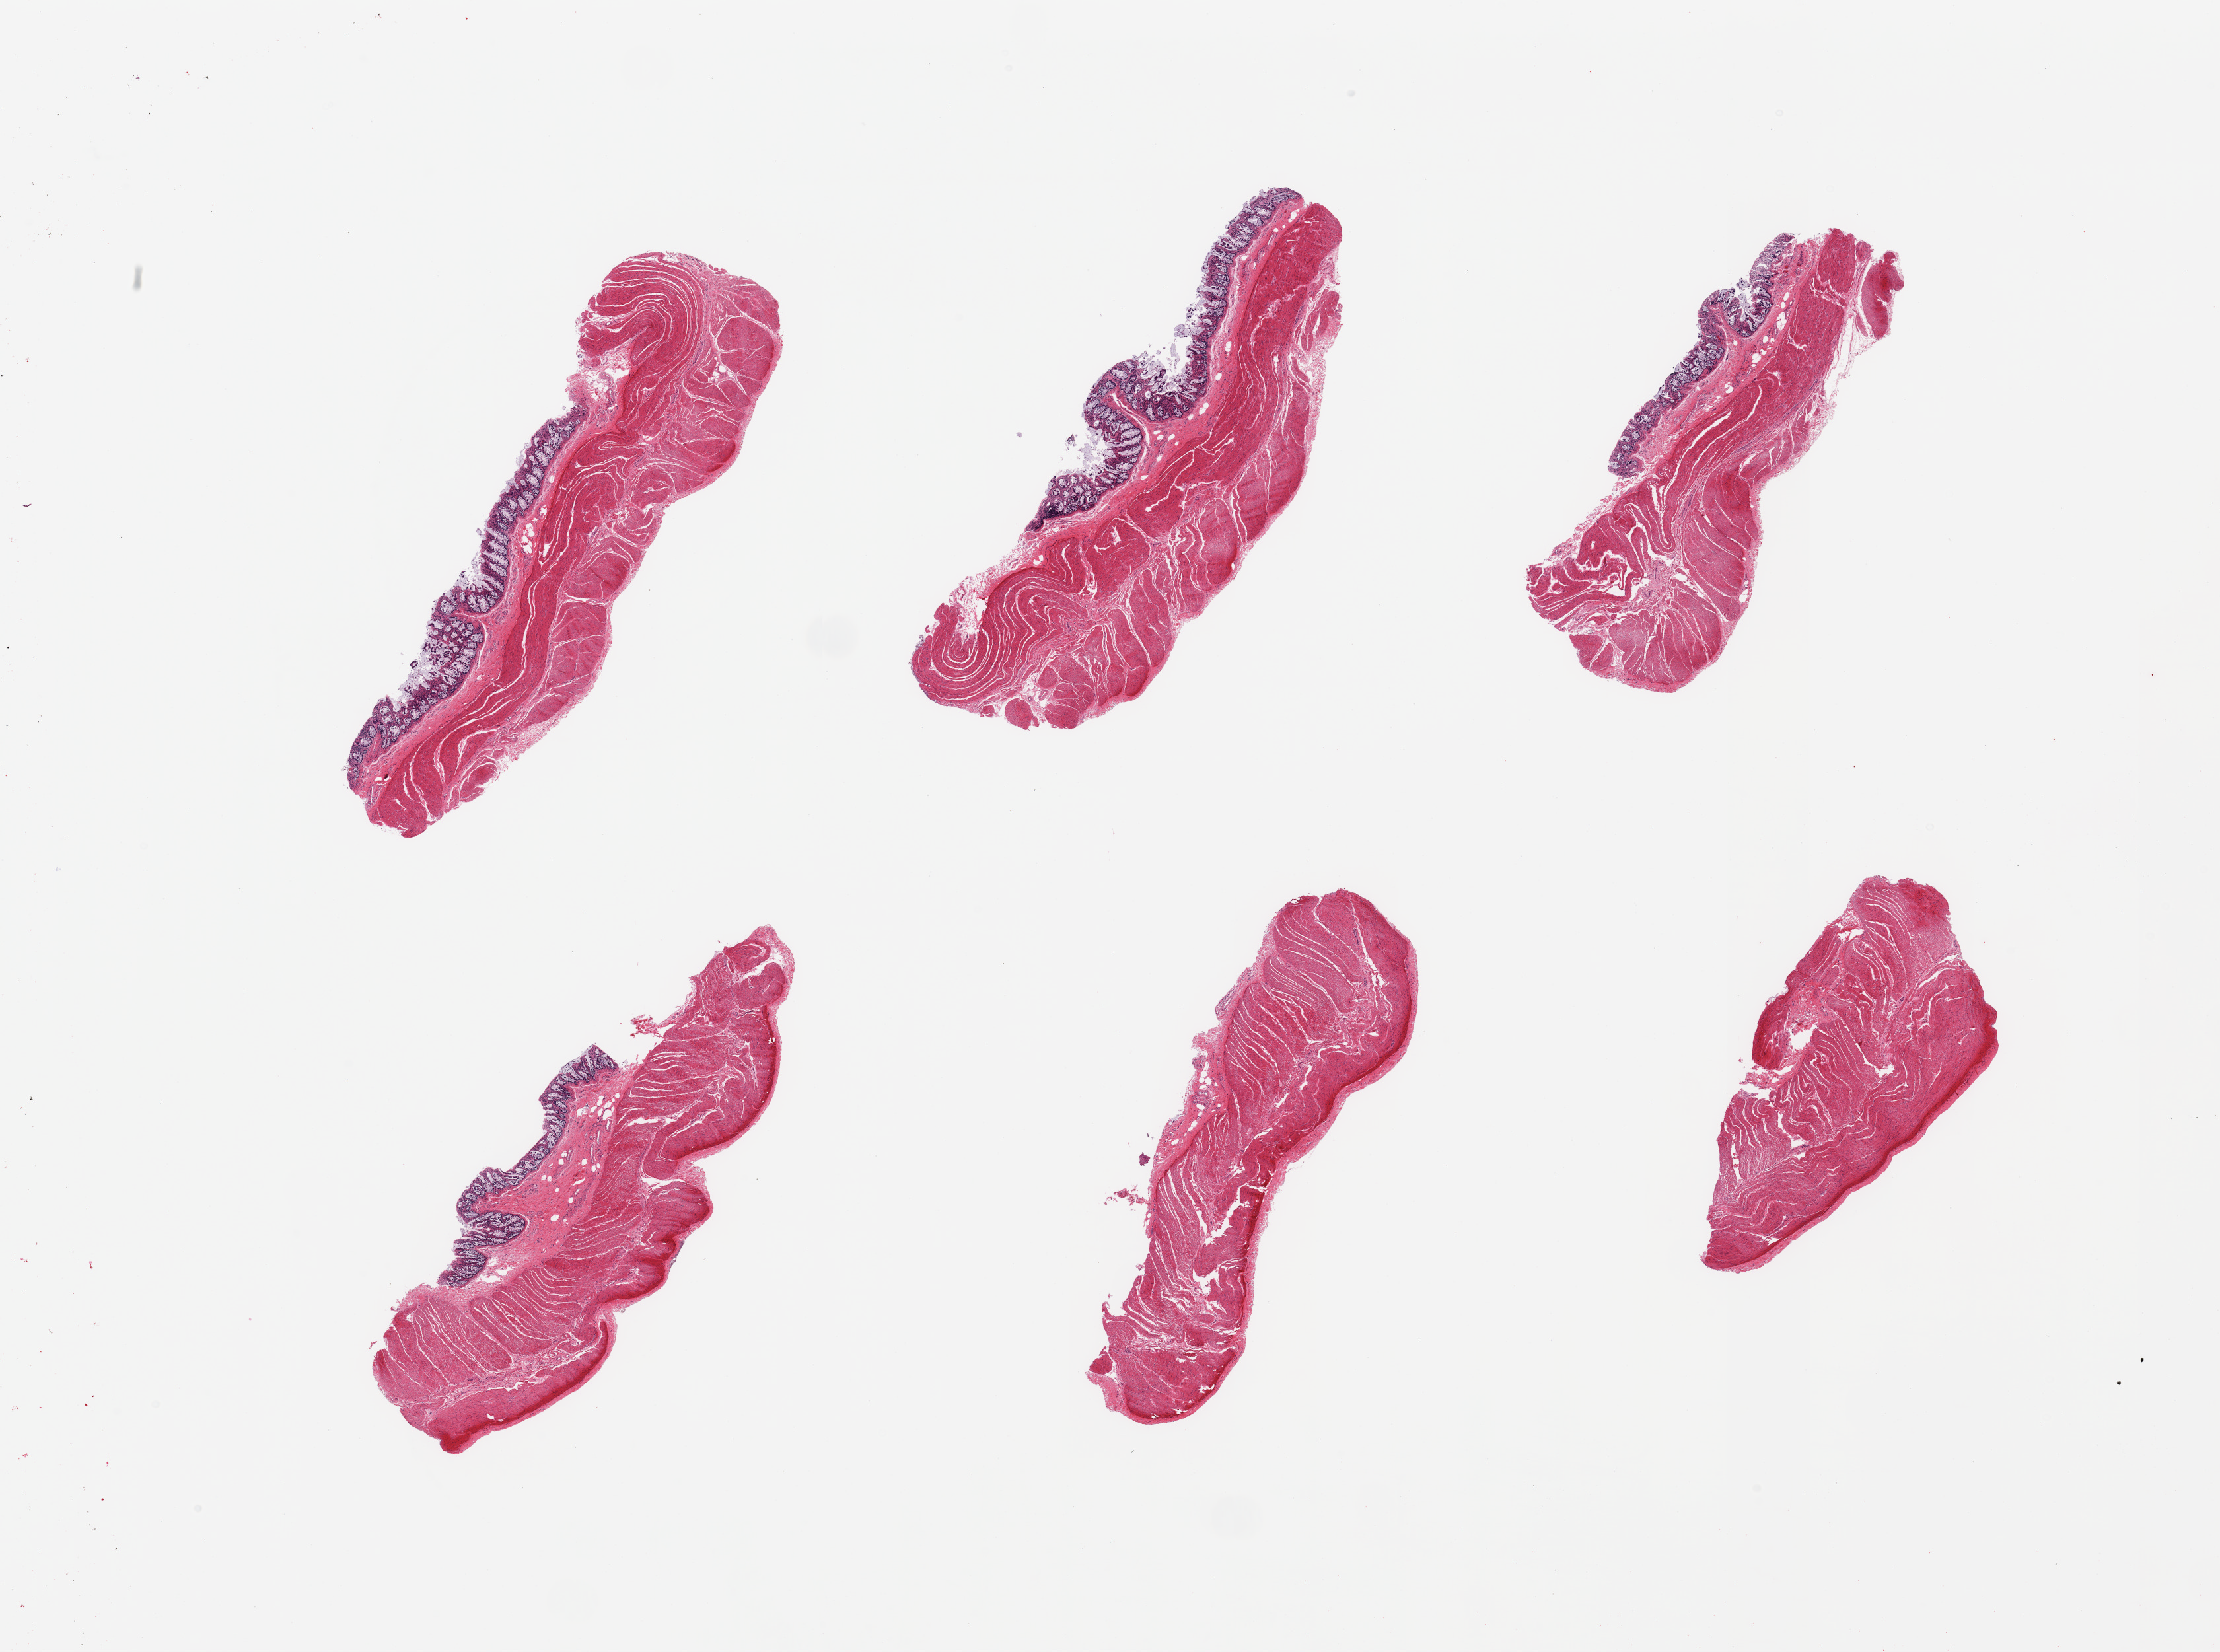
Digitized H&E-stained section, whole scanned area (about 26.6 x 19.8 mm, from a 20x scan) shown as a low-resolution overview. PAXgene-fixed, paraffin-embedded tissue. Sampled site (target tissue): transverse colon. Tissue donor sample. Male donor.
Reviewer comment on this tissue sample: 6 pieces, focally well-fixed mucosa, 0.3-0.4mm.